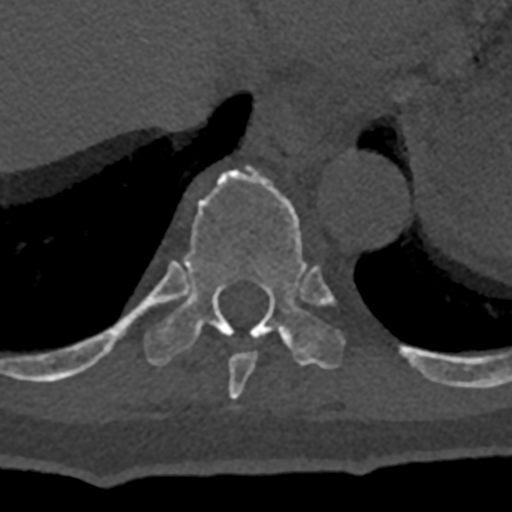
CT including the spine, one axial slice; slice 616 of 797 in the series (ordered by position); reconstruction kernel Br40s/3; 120 kVp; bone window (W 1800 / L 400 HU); 0.5 mm slice thickness; 512 × 512 image matrix, field of view 160 × 160 mm. Patient: male, 74 years. Case-level facts recorded for this patient, not image findings: primary cancer: renal; vertebrae with lytic lesions (as recorded): T10, L1, L2, L3, L4, L5.
Outlined on this slice (semi-automatic segmentation, software-assisted and operator-edited):
- T10 vertebra: box from (x=70, y=166) to (x=432, y=381) px
- T9 vertebra: (x=228, y=352)–(x=257, y=400)